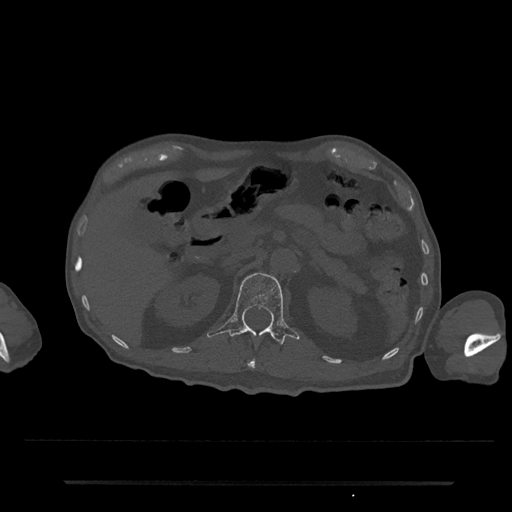
CT including the spine, one axial slice. Position 141 of 797 along the scan axis. 120 kVp. Bone window (W 1800 / L 400 HU). 512 × 512 image matrix, field of view 427 × 427 mm. Patient: male, 74 years. Case-level facts recorded for this patient, not image findings: primary cancer: prostate.
Structures marked on this image (semi-automatically segmented with operator editing):
- L1 vertebra: bounding box <207,272,300,346> (left, top, right, bottom; pixels)
- T12 vertebra: <247,360,256,369>